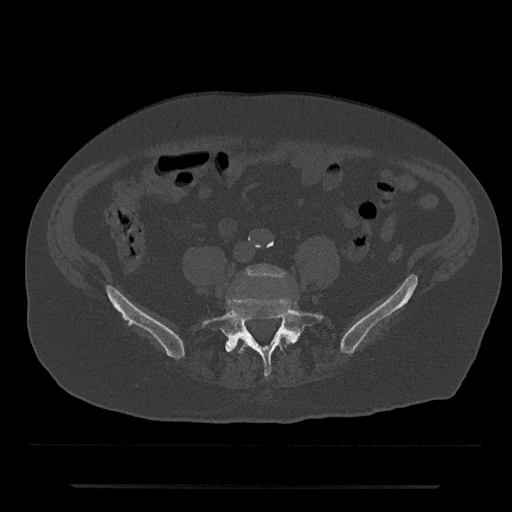
CT including the spine, one axial slice. Position 302 of 797 along the scan axis. 120 kVp. Bone window (W 1800 / L 400 HU). 0.5 mm slice thickness. 512 × 512 image matrix, field of view 434 × 434 mm. Patient: male, 80 years. From the clinical record (not read from this slice): primary cancer: prostate; vertebrae with lytic lesions (as recorded): L1, T11.
Structures marked on this image (semi-automatically segmented with operator editing):
- L4 vertebra: bounding box <244,265,286,280> (left, top, right, bottom; pixels)
- L5 vertebra: <201,297,323,377>